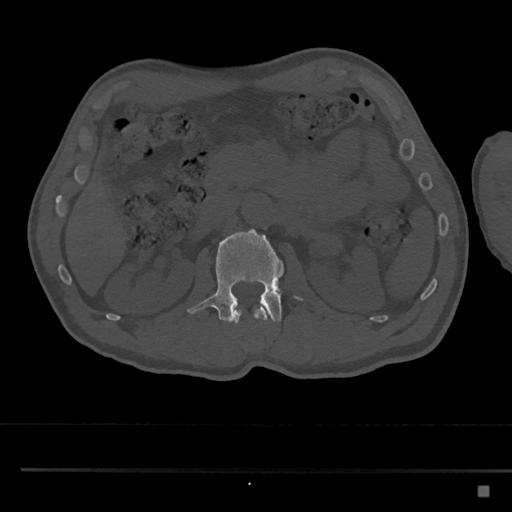
CT including the spine, one axial slice; slice 778 of 797 in the series (ordered by position); reconstruction kernel Br40s/3; 120 kVp; bone window (W 1800 / L 400 HU); 0.5 mm slice thickness; 512 × 512 image matrix, field of view 391 × 391 mm. Patient: male, 59 years. Case-level facts recorded for this patient, not image findings: primary cancer: prostate.
Outlined on this slice (semi-automatic segmentation, software-assisted and operator-edited):
- L1 vertebra: bounding box [x1, y1, x2, y2] px = [232, 307, 269, 323]
- L2 vertebra: [187, 229, 303, 322]